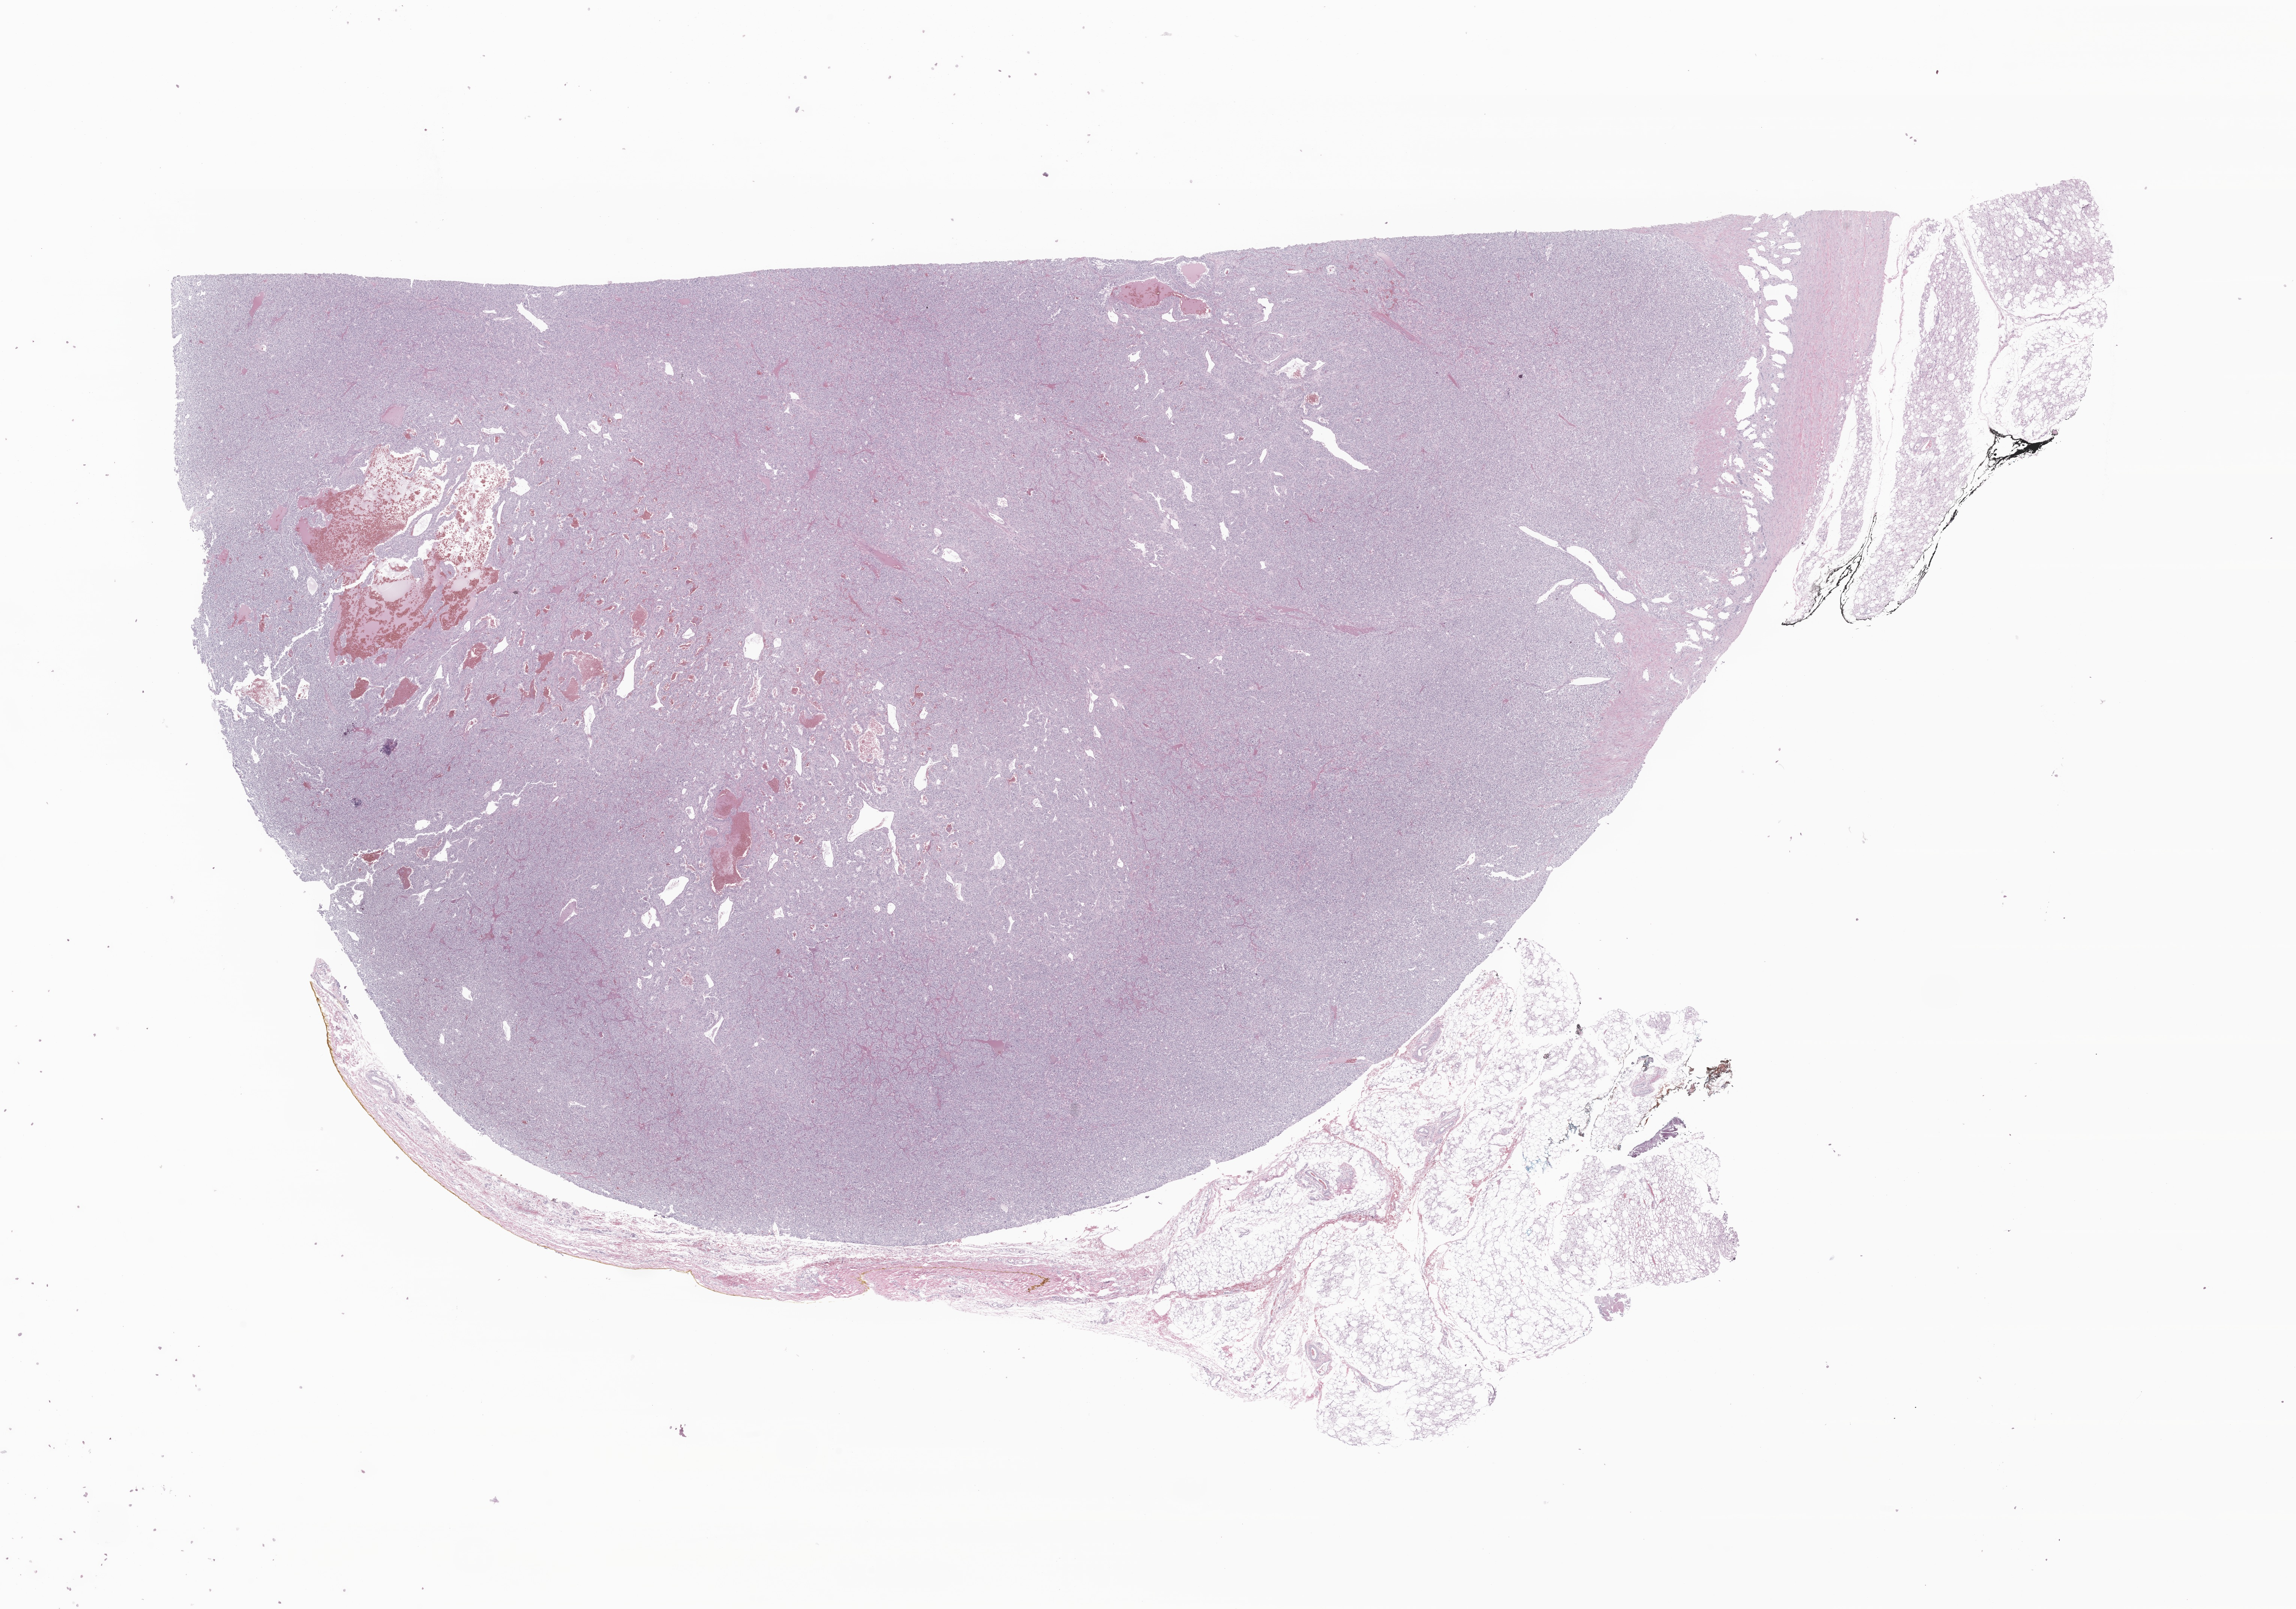
Whole-slide image, haematoxylin and eosin stain of tumor tissue from the adrenal gland, a low-resolution overview of the entire scanned area, about 25.8 x 18.1 mm; FFPE section. Patient male; age 127 months.
• diagnosis: Pheochromocytoma, NOS